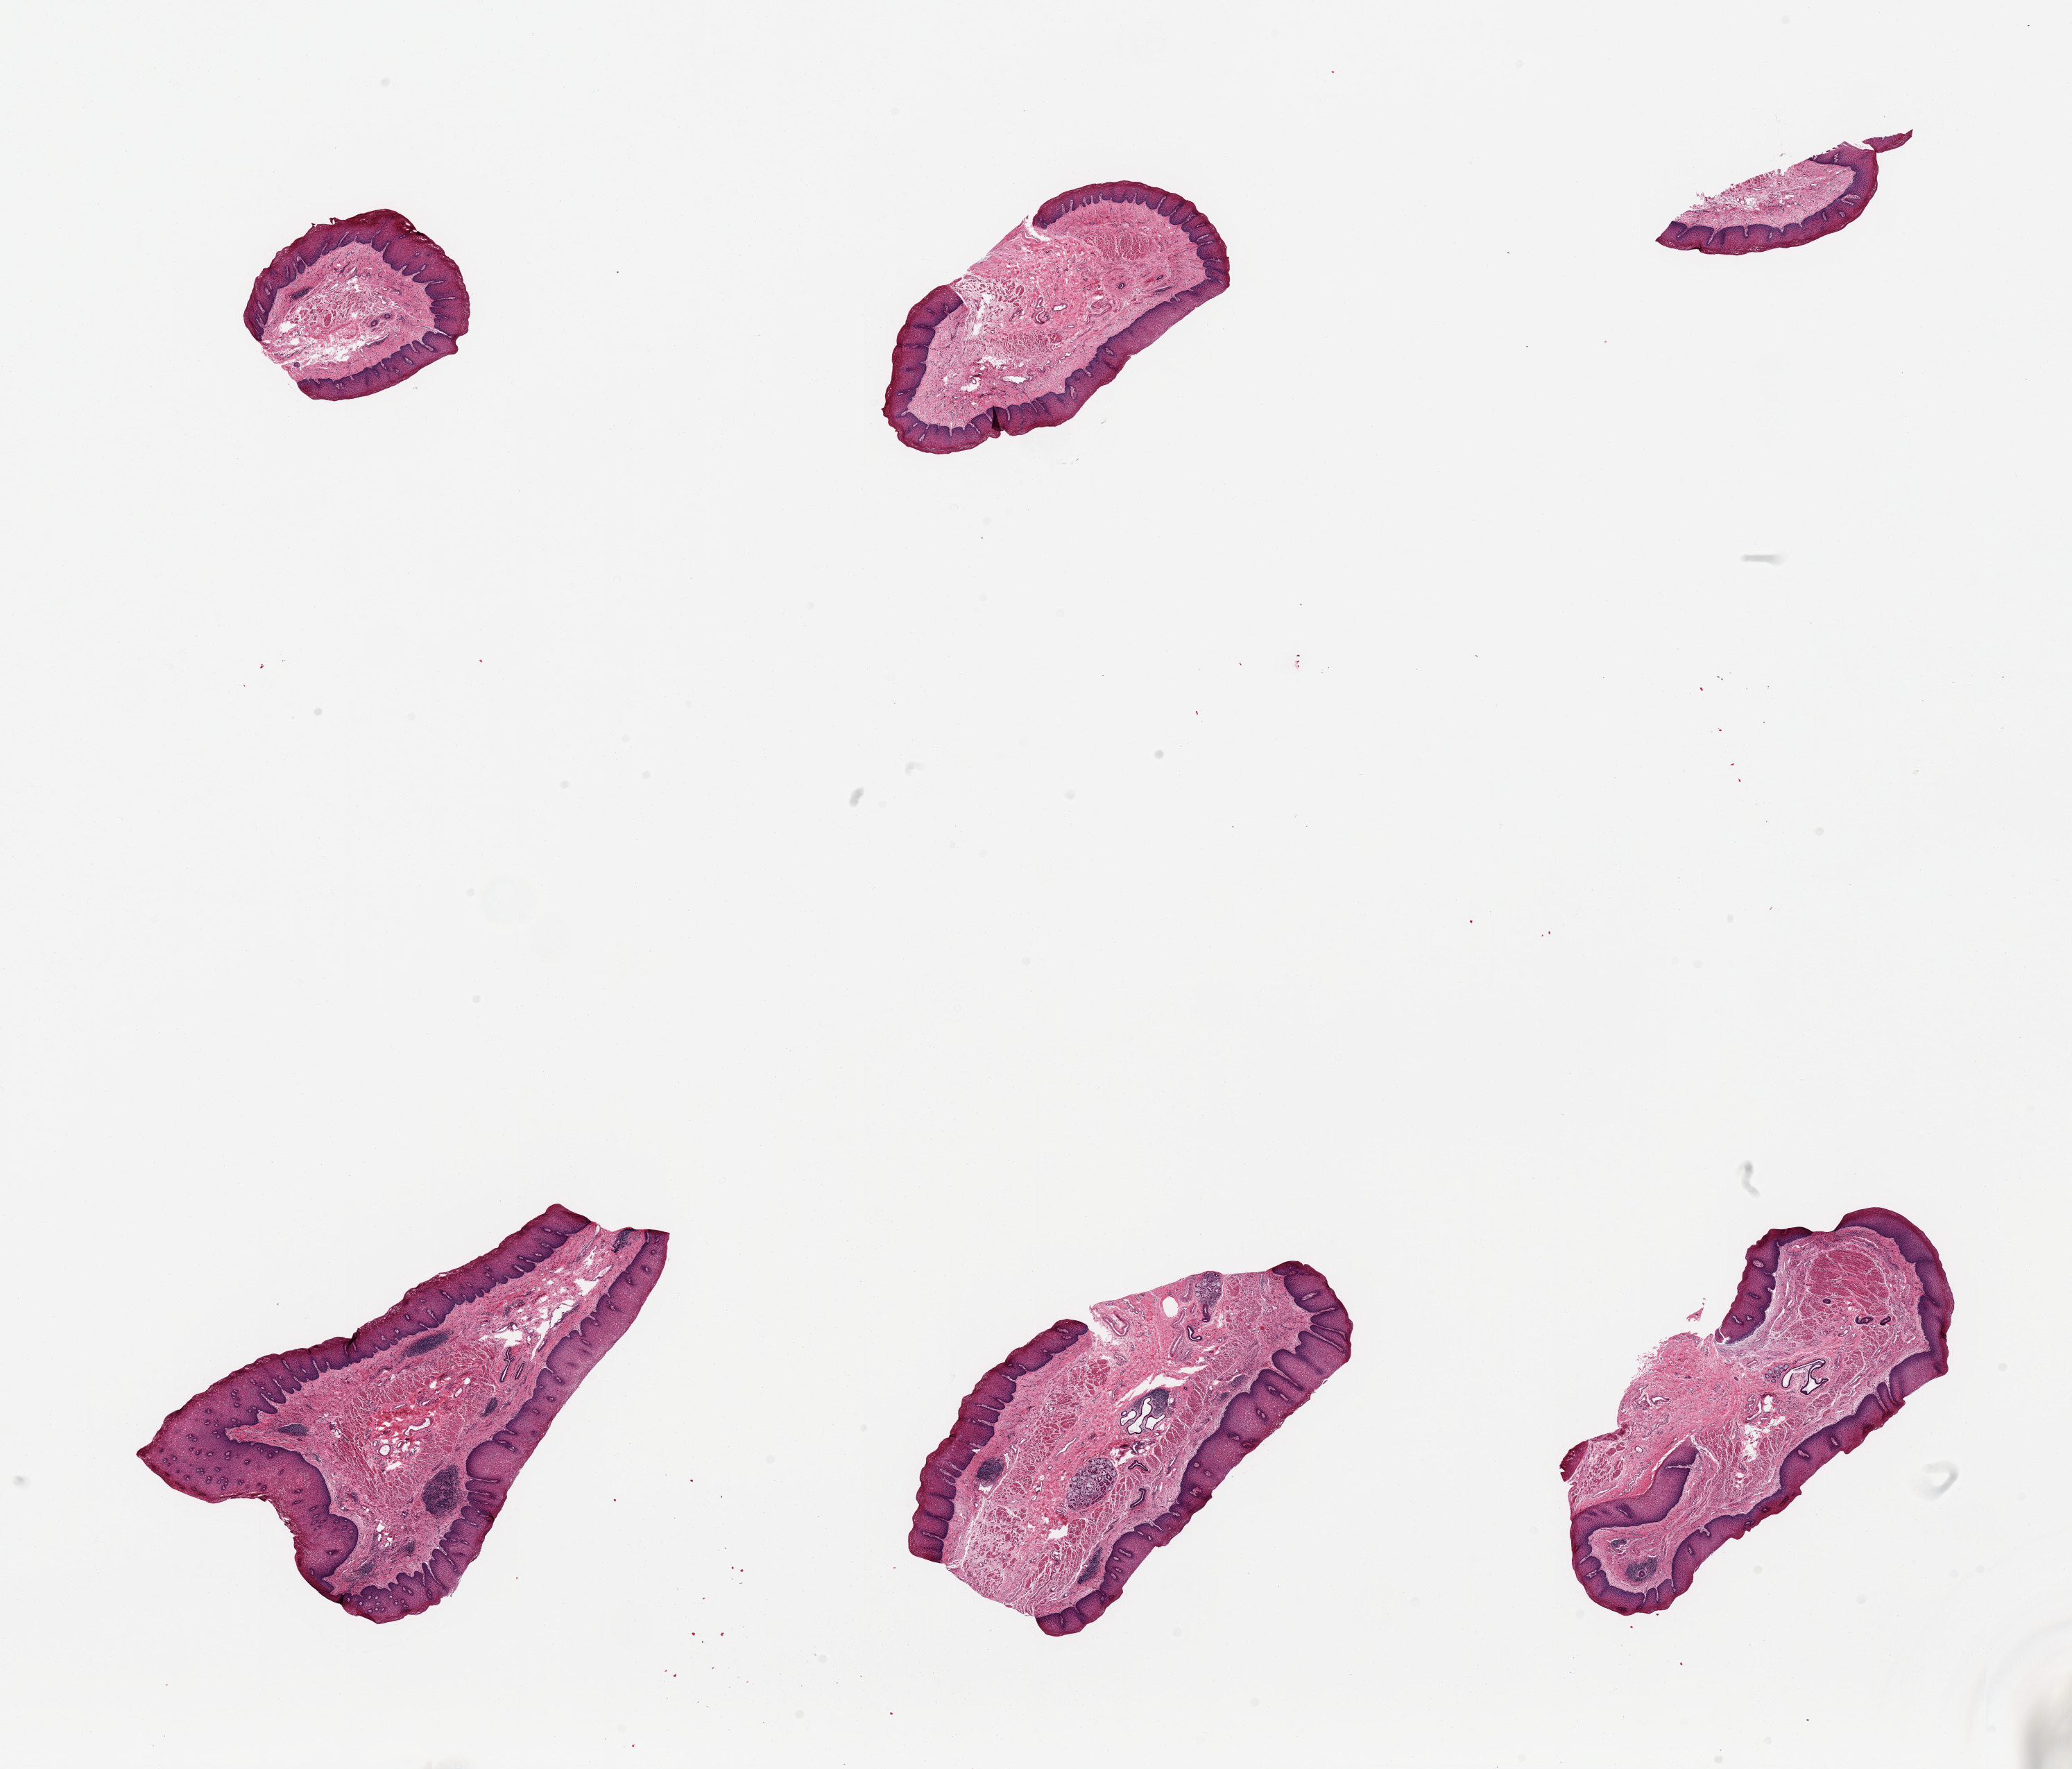
Digitized hematoxylin and eosin (H&E)-stained section — whole scanned area (about 23.6 x 20.2 mm, acquisition: 20x scan) shown as a low-resolution overview, PAXgene-fixed paraffin-embedded (PFPE) section, target tissue: esophageal mucous membrane, donor tissue sample.
Pathologist's review note for this sample: 6 pieces; moderate squamous hyperplasia.